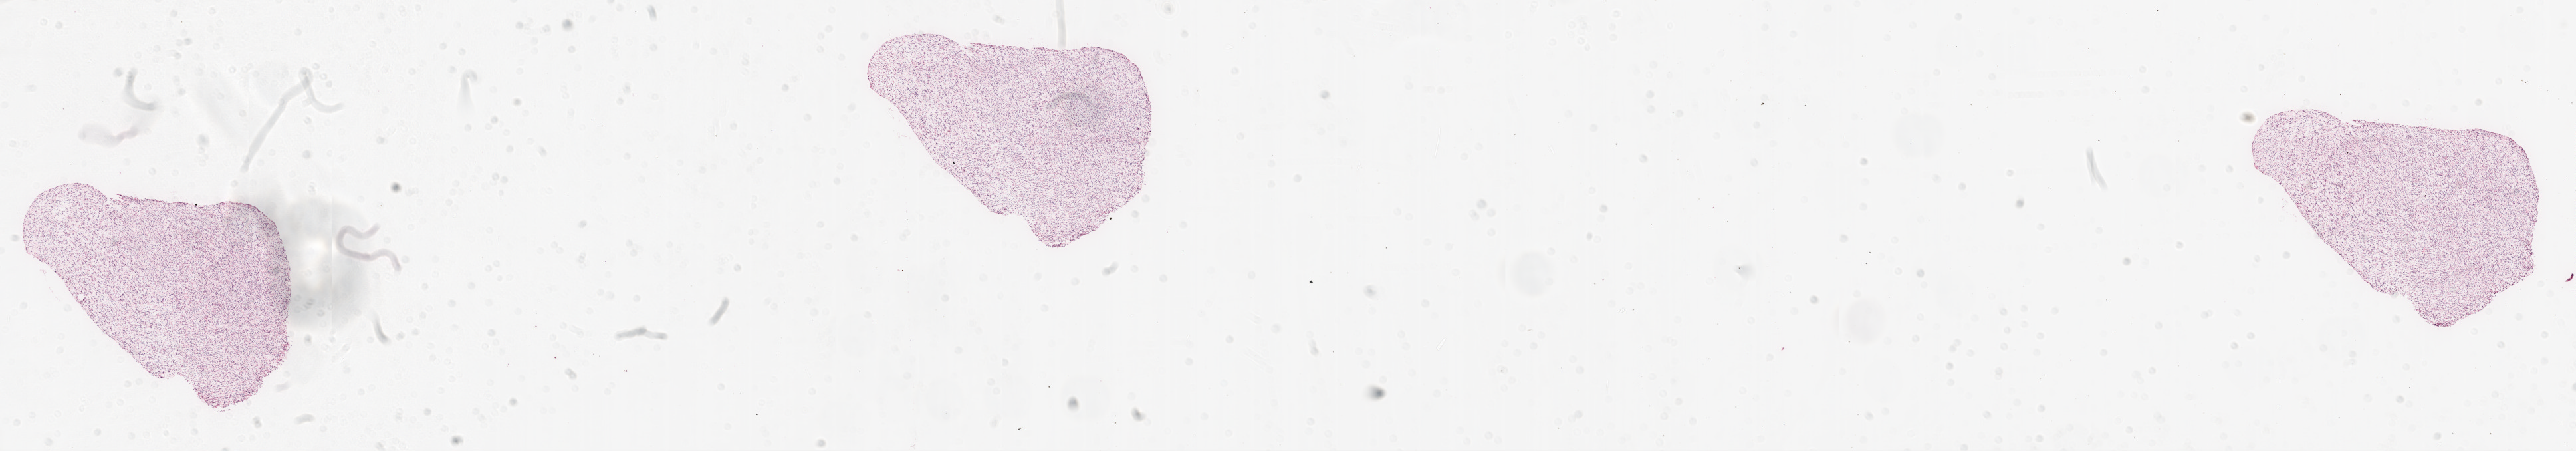
Whole-slide histology image, H&E-stained — whole scanned area (about 31.1 x 5.4 mm) shown as a low-resolution overview. Frozen section from the top of the tissue portion. Primary tumour sample from the brain. Female patient; age at initial diagnosis 82 years. Pathologist review of this section (percent, as recorded): tumour cells 95%, tumour nuclei 95%, normal cells 0%, stromal cells 5%, necrosis 0%.
- diagnosis: Glioblastoma